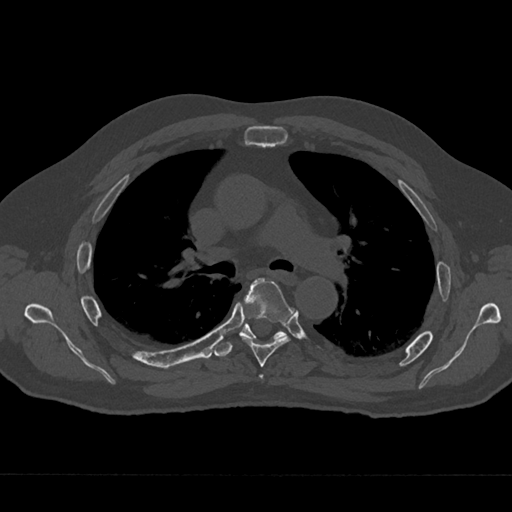
CT including the spine, one axial slice; 120 kVp; bone window (W 1800 / L 400 HU); 0.5 mm slice thickness; 512 × 512 image matrix, field of view 377 × 377 mm. Patient: male, 75 years. From the clinical record (not read from this slice): primary cancer: renal; vertebrae with lytic lesions (as recorded): T4.
Outlined on this slice (semi-automatic segmentation, software-assisted and operator-edited):
- T4 vertebra: box from (x=259, y=374) to (x=263, y=379) px
- T5 vertebra: (x=240, y=278)–(x=293, y=367)
- T6 vertebra: (x=215, y=318)–(x=287, y=357)